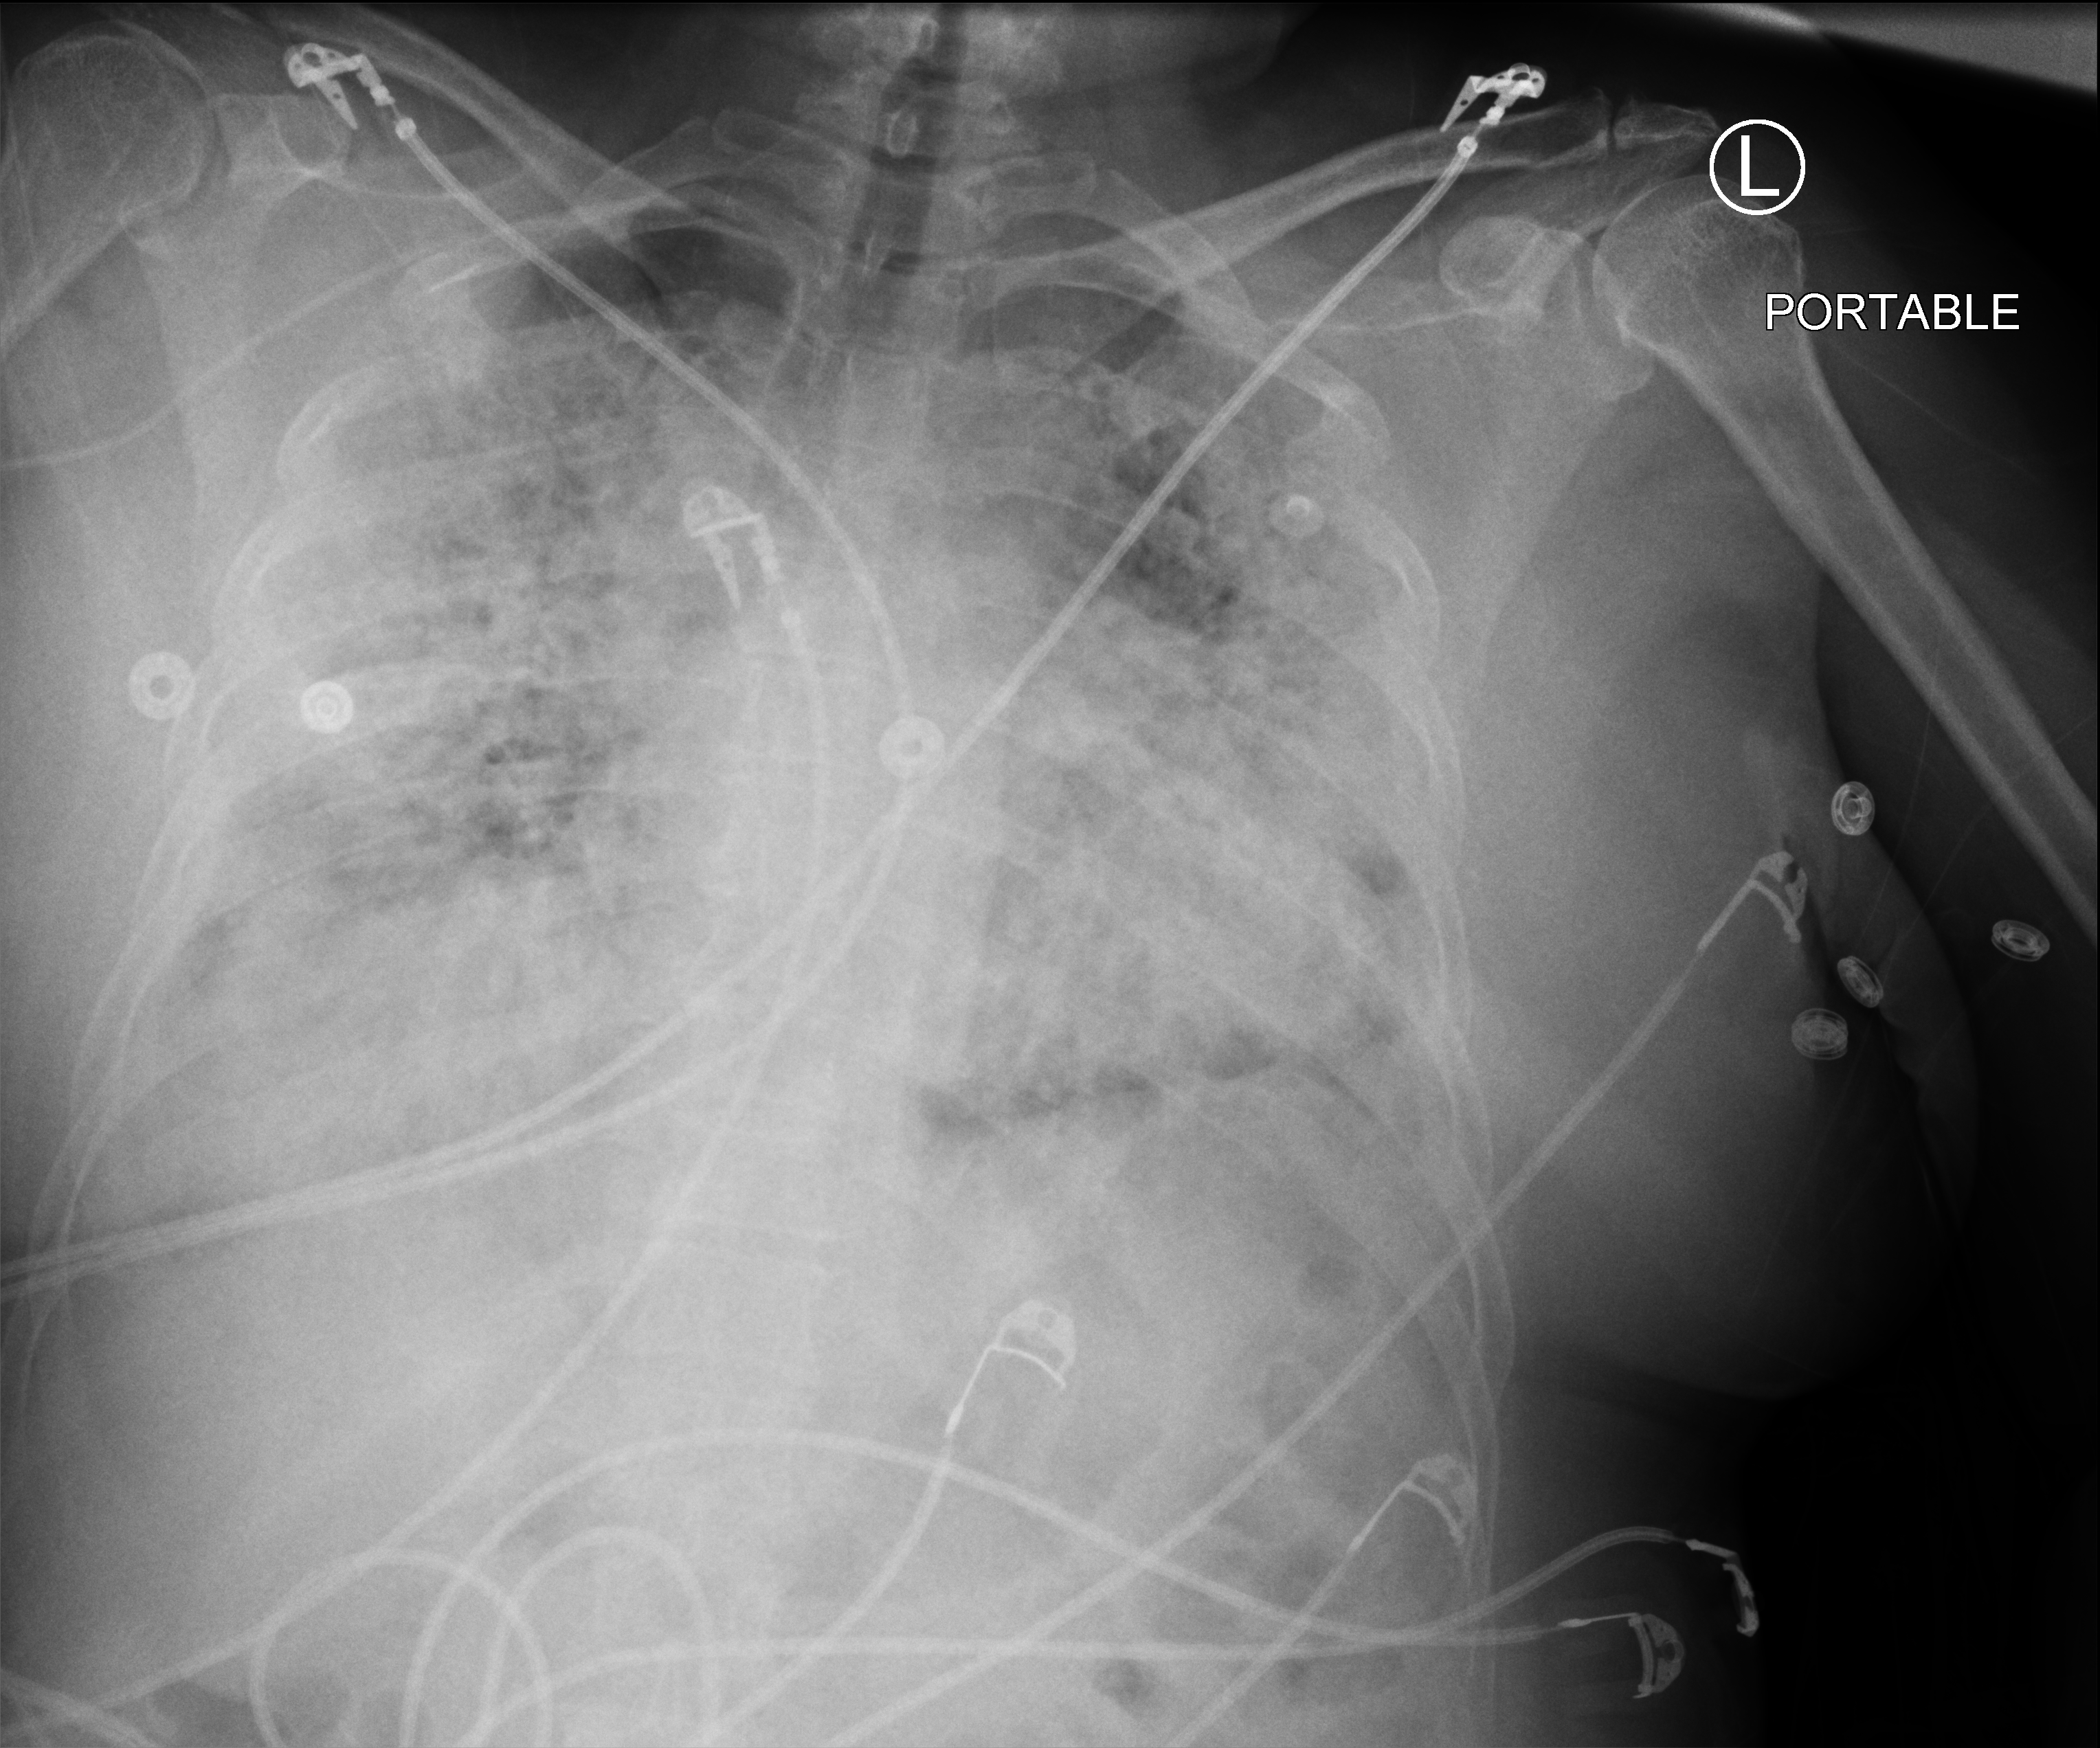
Portable chest radiograph, anteroposterior (AP) projection. Patient hospitalised with COVID-19; female, aged 18–59 years.
From the hospital-stay record, not from the radiograph (when in the stay this image was taken is not recorded):
- admitted to intensive care during this hospital stay: no
- mechanically ventilated during this hospital stay: no